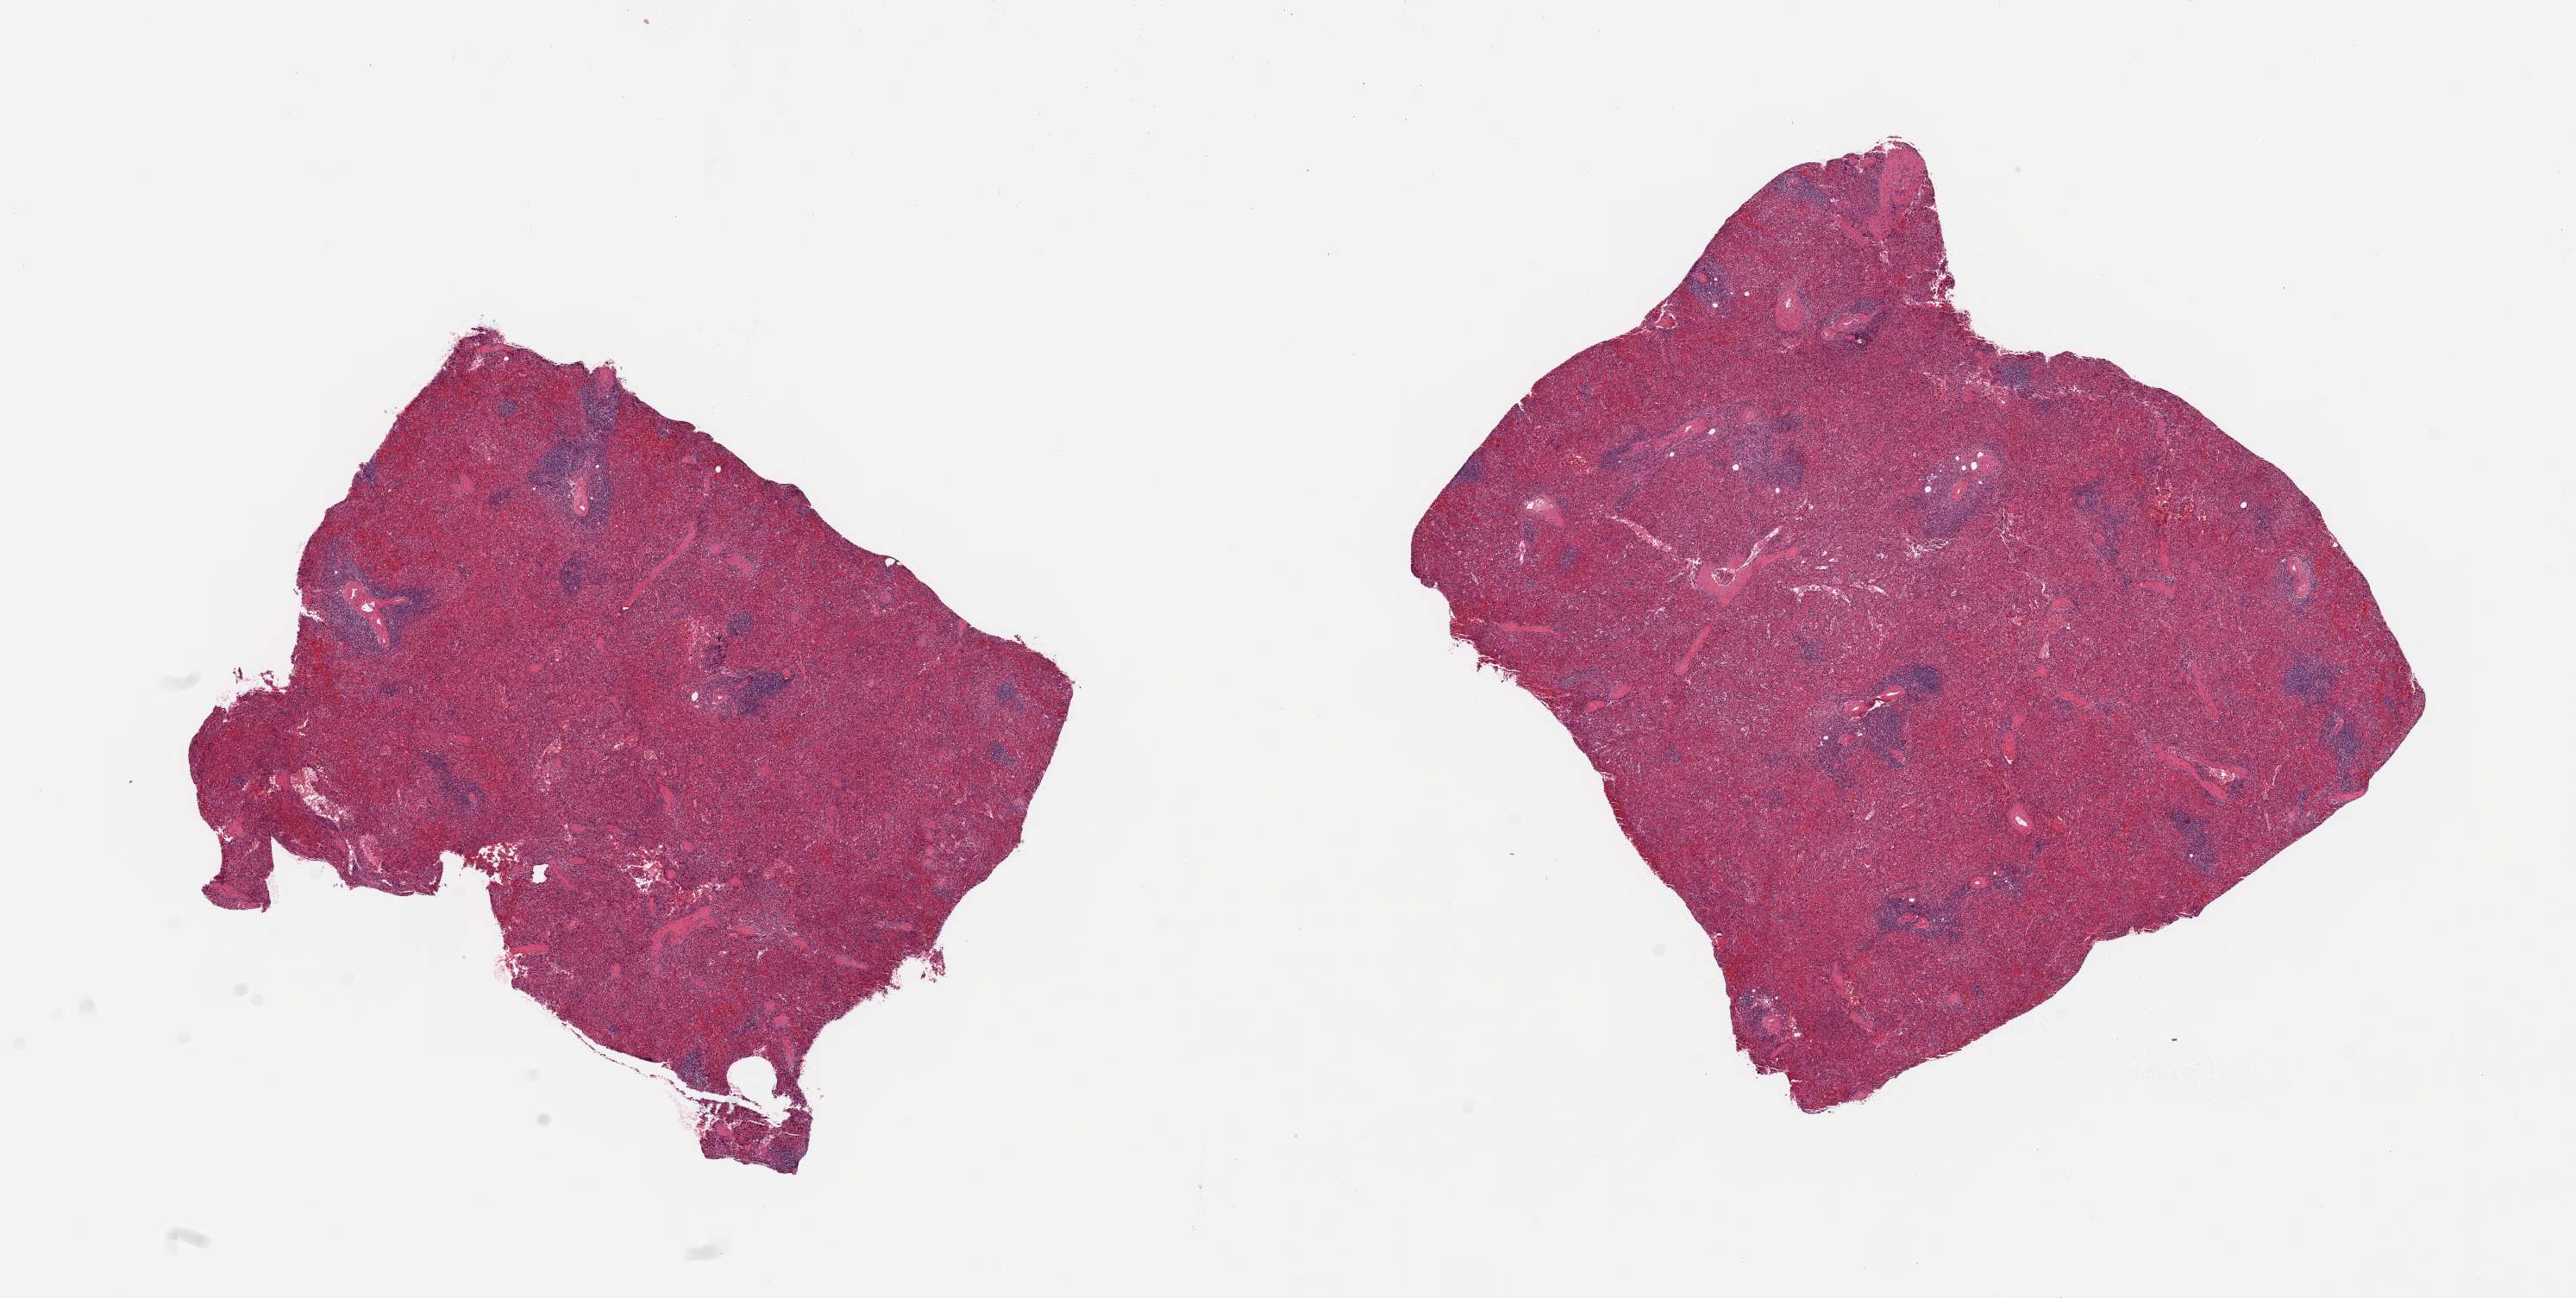
Digitized hematoxylin and eosin (H&E)-stained section — shown as a low-resolution overview of the whole scanned area (about 23.6 x 11.9 mm, slide scanned at 20x); PAXgene-fixed, paraffin-embedded tissue; sampled site (target tissue): spleen; tissue donor sample. Donor: female.
- reviewer comment on this tissue sample: 2 pieces